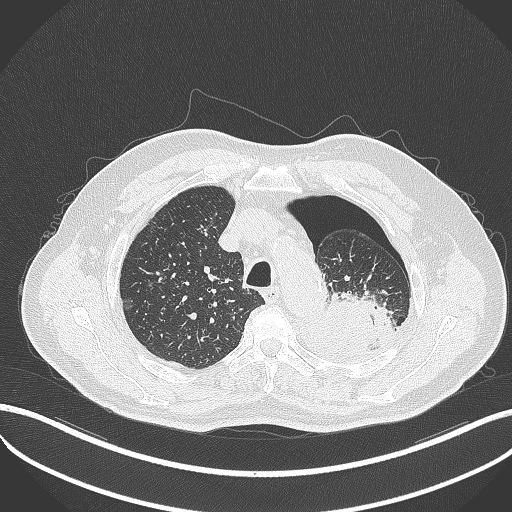
Chest CT, one axial slice; slice 397 of 464 in the series (ordered by position); reconstruction kernel B70f; lung window (W 1500 / L -600 HU); 1 mm slice thickness; 512 × 512 image matrix, field of view 400 × 400 mm. Male patient, age 76 years. Case-level facts recorded for this patient, not image findings: clinical TNM (as recorded): T3 N0 M1b.
Structures marked on this image (bounding box drawn by a radiologist):
- lung tumour (recorded histology: adenocarcinoma): box from (x=314, y=290) to (x=398, y=359) px